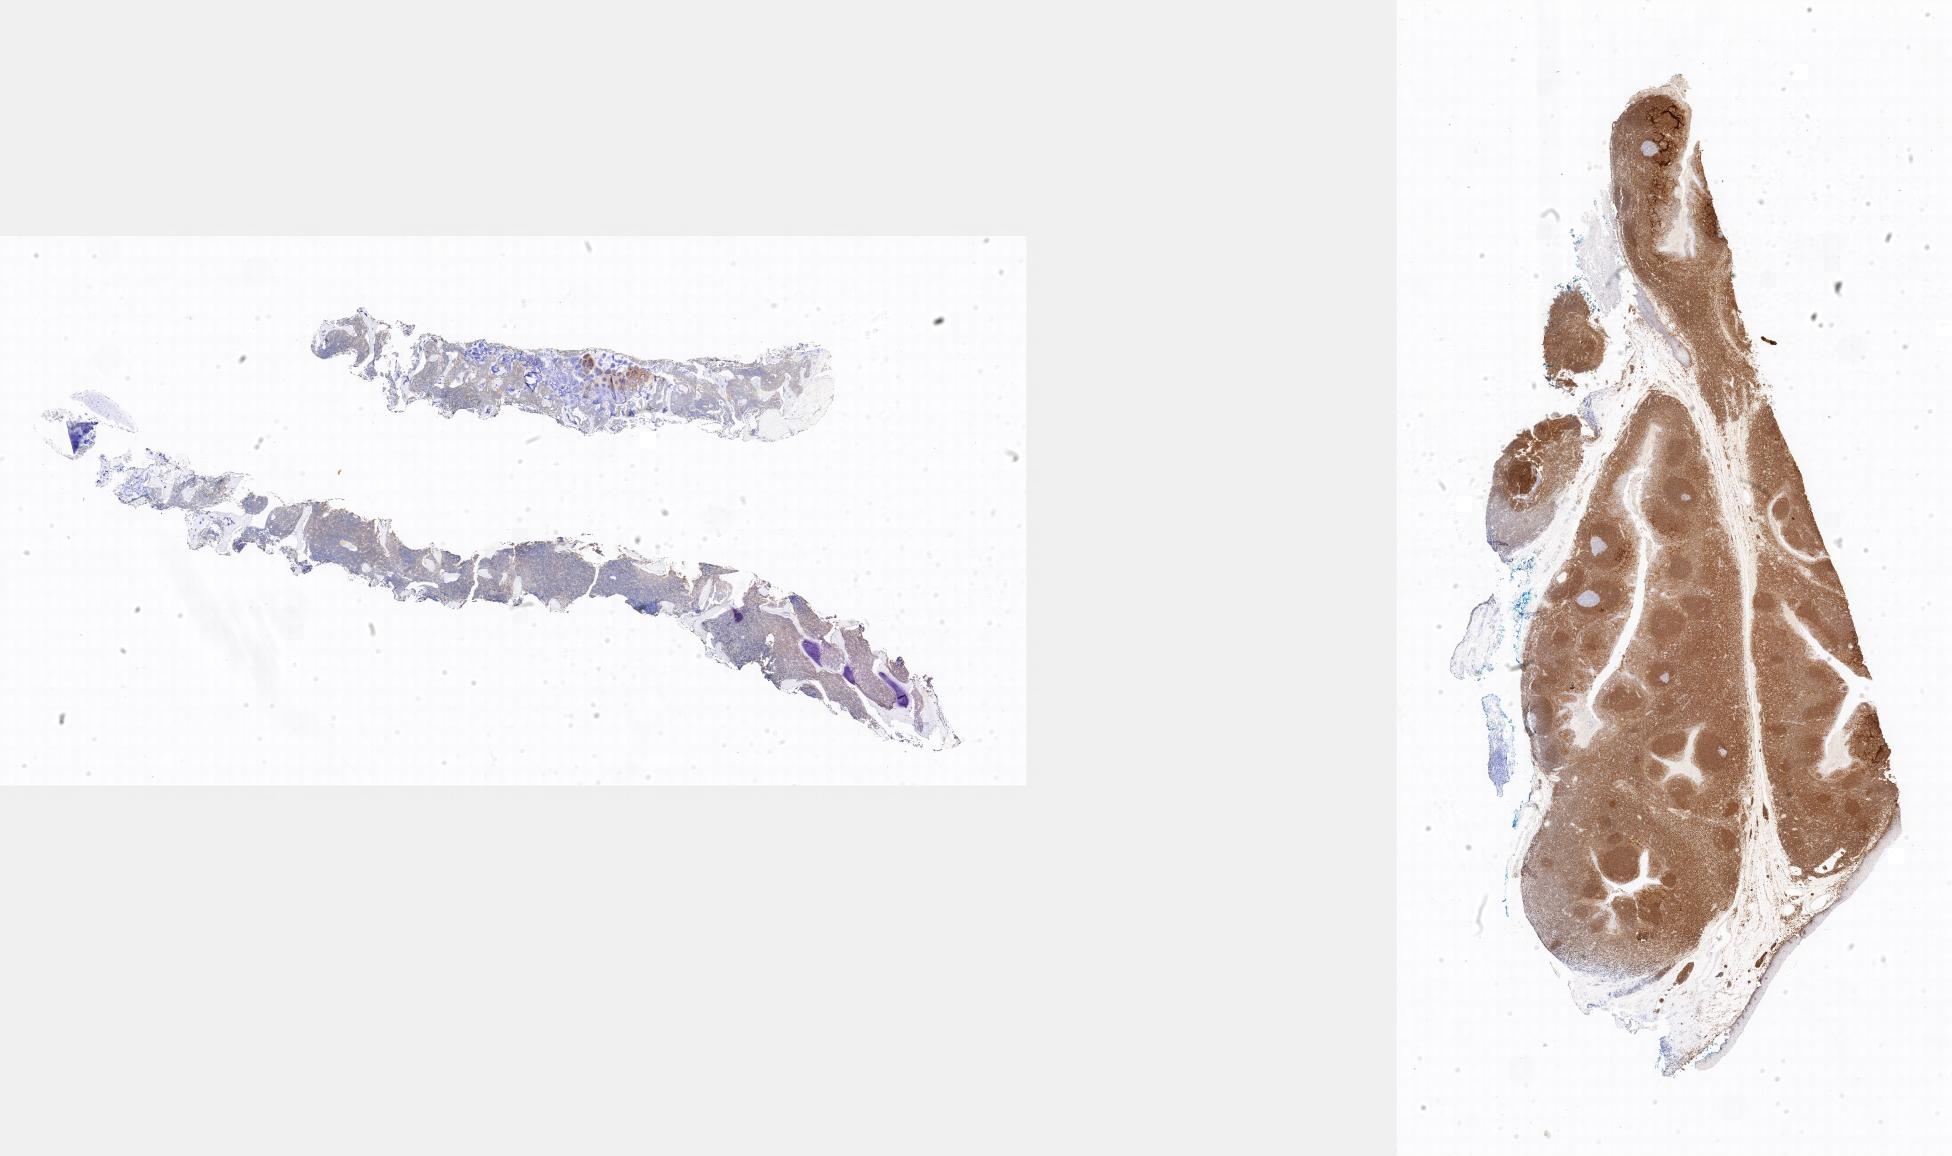
IHC for BCL2, whole-slide image, whole scanned area shown as a low-resolution overview; tumor tissue; anatomic site: bone marrow. Male patient, age 11 years.
Diagnosis: Burkitt lymphoma, NOS.